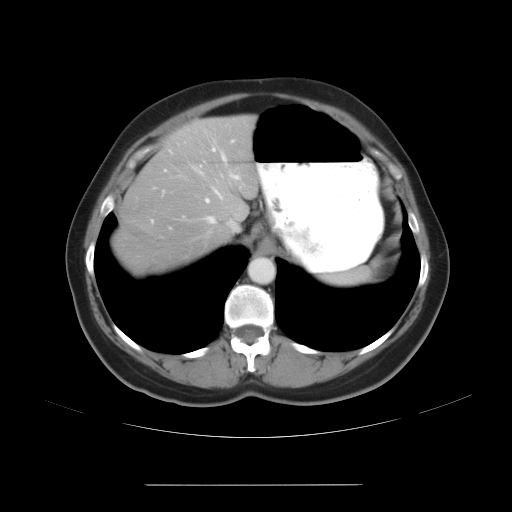
Contrast-enhanced abdominal CT, one axial slice. Position 22 of 27 along the scan axis. Reconstruction kernel STANDARD. Intravenous contrast given. Soft-tissue window (W 400 / L 40 HU). 512 × 512 image matrix. Female patient, age 58 years. Case-level facts recorded for this patient, not image findings: diagnosis: colorectal cancer liver metastases, imaged before liver resection; multiple liver metastases: yes; largest metastasis: 1.9 cm.
Outlined on this slice (outlined manually by an expert reader):
- hepatic veins: box from (x=193, y=154) to (x=240, y=229) px
- liver: (x=122, y=118)–(x=257, y=265)
- planned liver remnant (the part of the liver to remain after resection): (x=126, y=118)–(x=257, y=228)
- portal vein (with intrahepatic branches): (x=152, y=139)–(x=217, y=222)